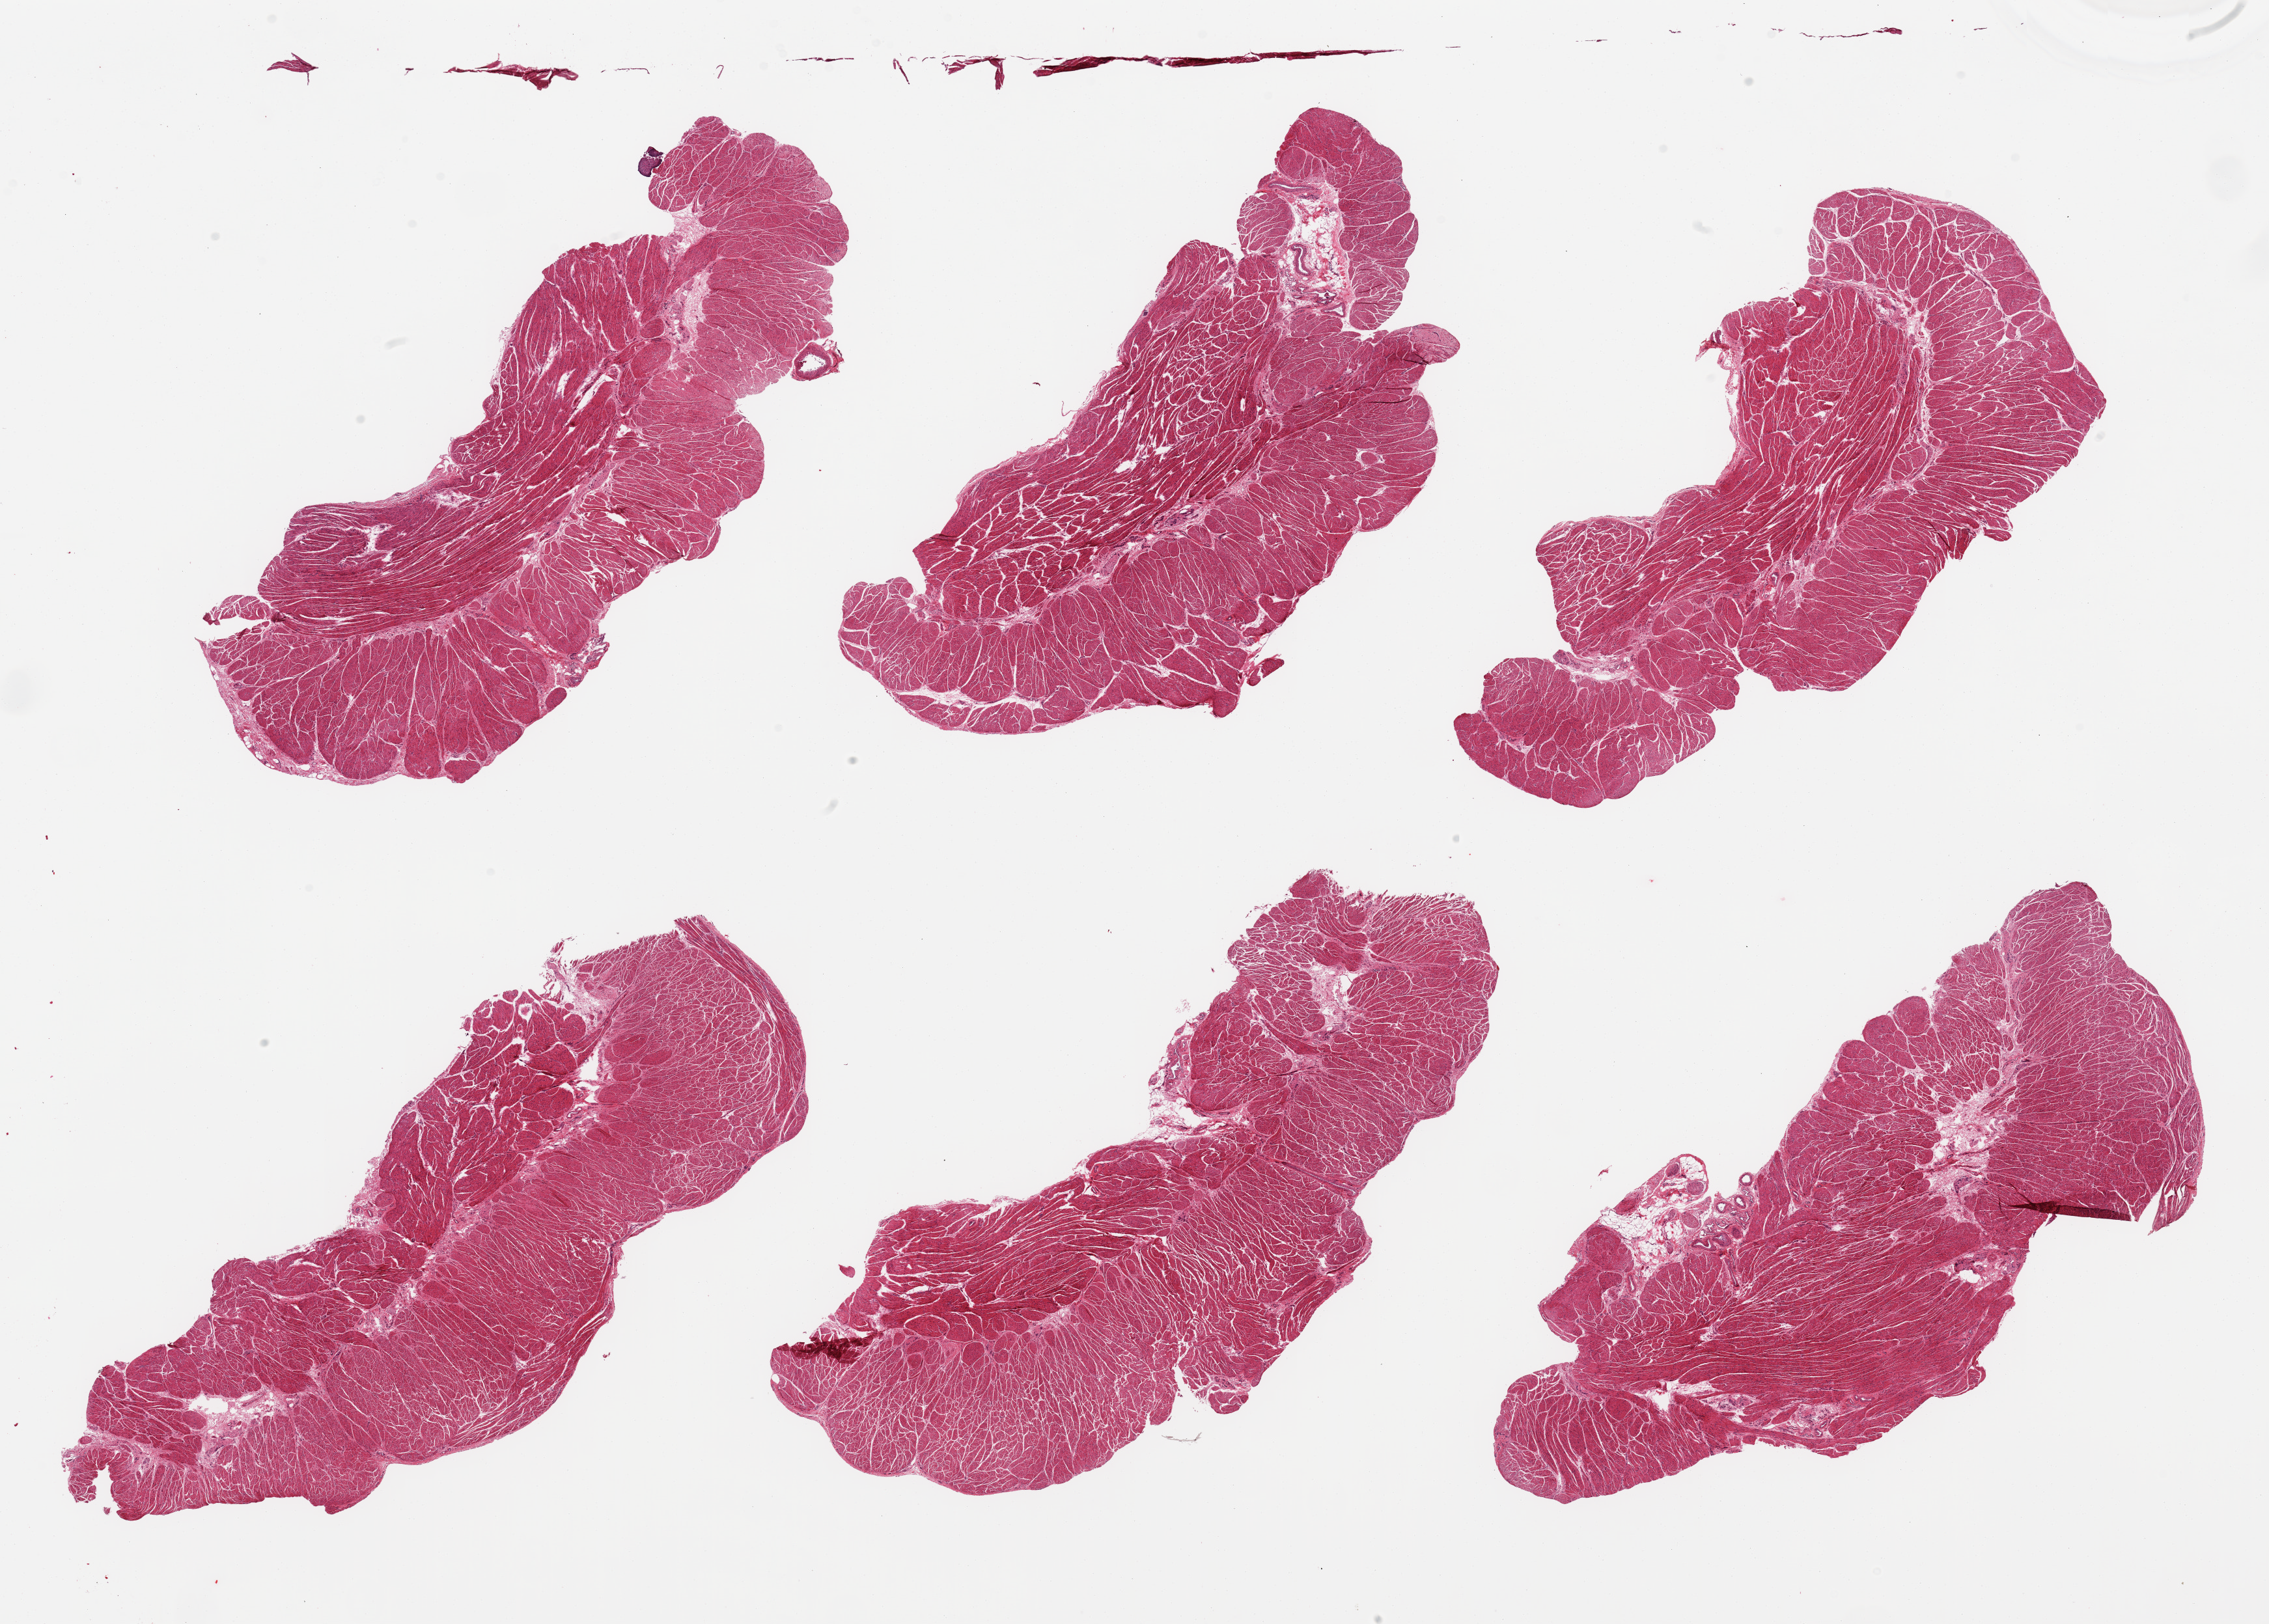
Digitized hematoxylin and eosin (H&E)-stained section, brightfield, shown as a low-resolution overview of the whole scanned area (about 27.6 x 19.7 mm, slide scanned at 20x); PAXgene-fixed, paraffin-embedded tissue; section of esophageal muscle (target tissue); donor tissue sample. Donor sex: female.
Reviewer comment on this tissue sample: 6 pieces; well trimmed target muscularis.